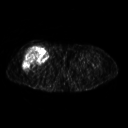
FDG PET of an extremity soft-tissue mass (from a PET/CT study), one axial slice. Position 263 of 311 along the scan axis. 3.27 mm slice thickness. 128 × 128 image matrix, field of view 500 × 500 mm. Female patient, age 57 years. Case-level facts recorded for this patient, not image findings: histological type: pleiomorphic undifferentiated sarcoma; grade: high; site of the primary tumour: right quadricep.
Outlined on this slice (expert contour drawn on MRI and transferred to this co-registered scan by the dataset authors):
- tumour plus oedema (research contour): bounding box (x1, y1, x2, y2) in pixels: (22, 46, 48, 71)
- tumour (research contour): (22, 46, 48, 71)